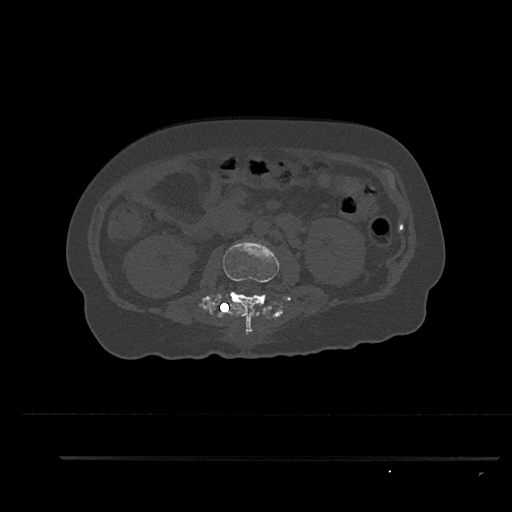
CT including the spine, one axial slice; slice 141 of 797 in the series (ordered by position); 120 kVp; bone window (W 1800 / L 400 HU); 0.5 mm slice thickness; 512 × 512 image matrix, field of view 408 × 408 mm. Female patient, age 44 years. From the clinical record (not read from this slice): primary cancer: renal; vertebrae with lytic lesions (as recorded): L1.
Annotated regions visible in this slice (semi-automatic segmentation, software-assisted and operator-edited):
- L2 vertebra: bounding box (x1, y1, x2, y2) in pixels: (198, 240, 280, 335)